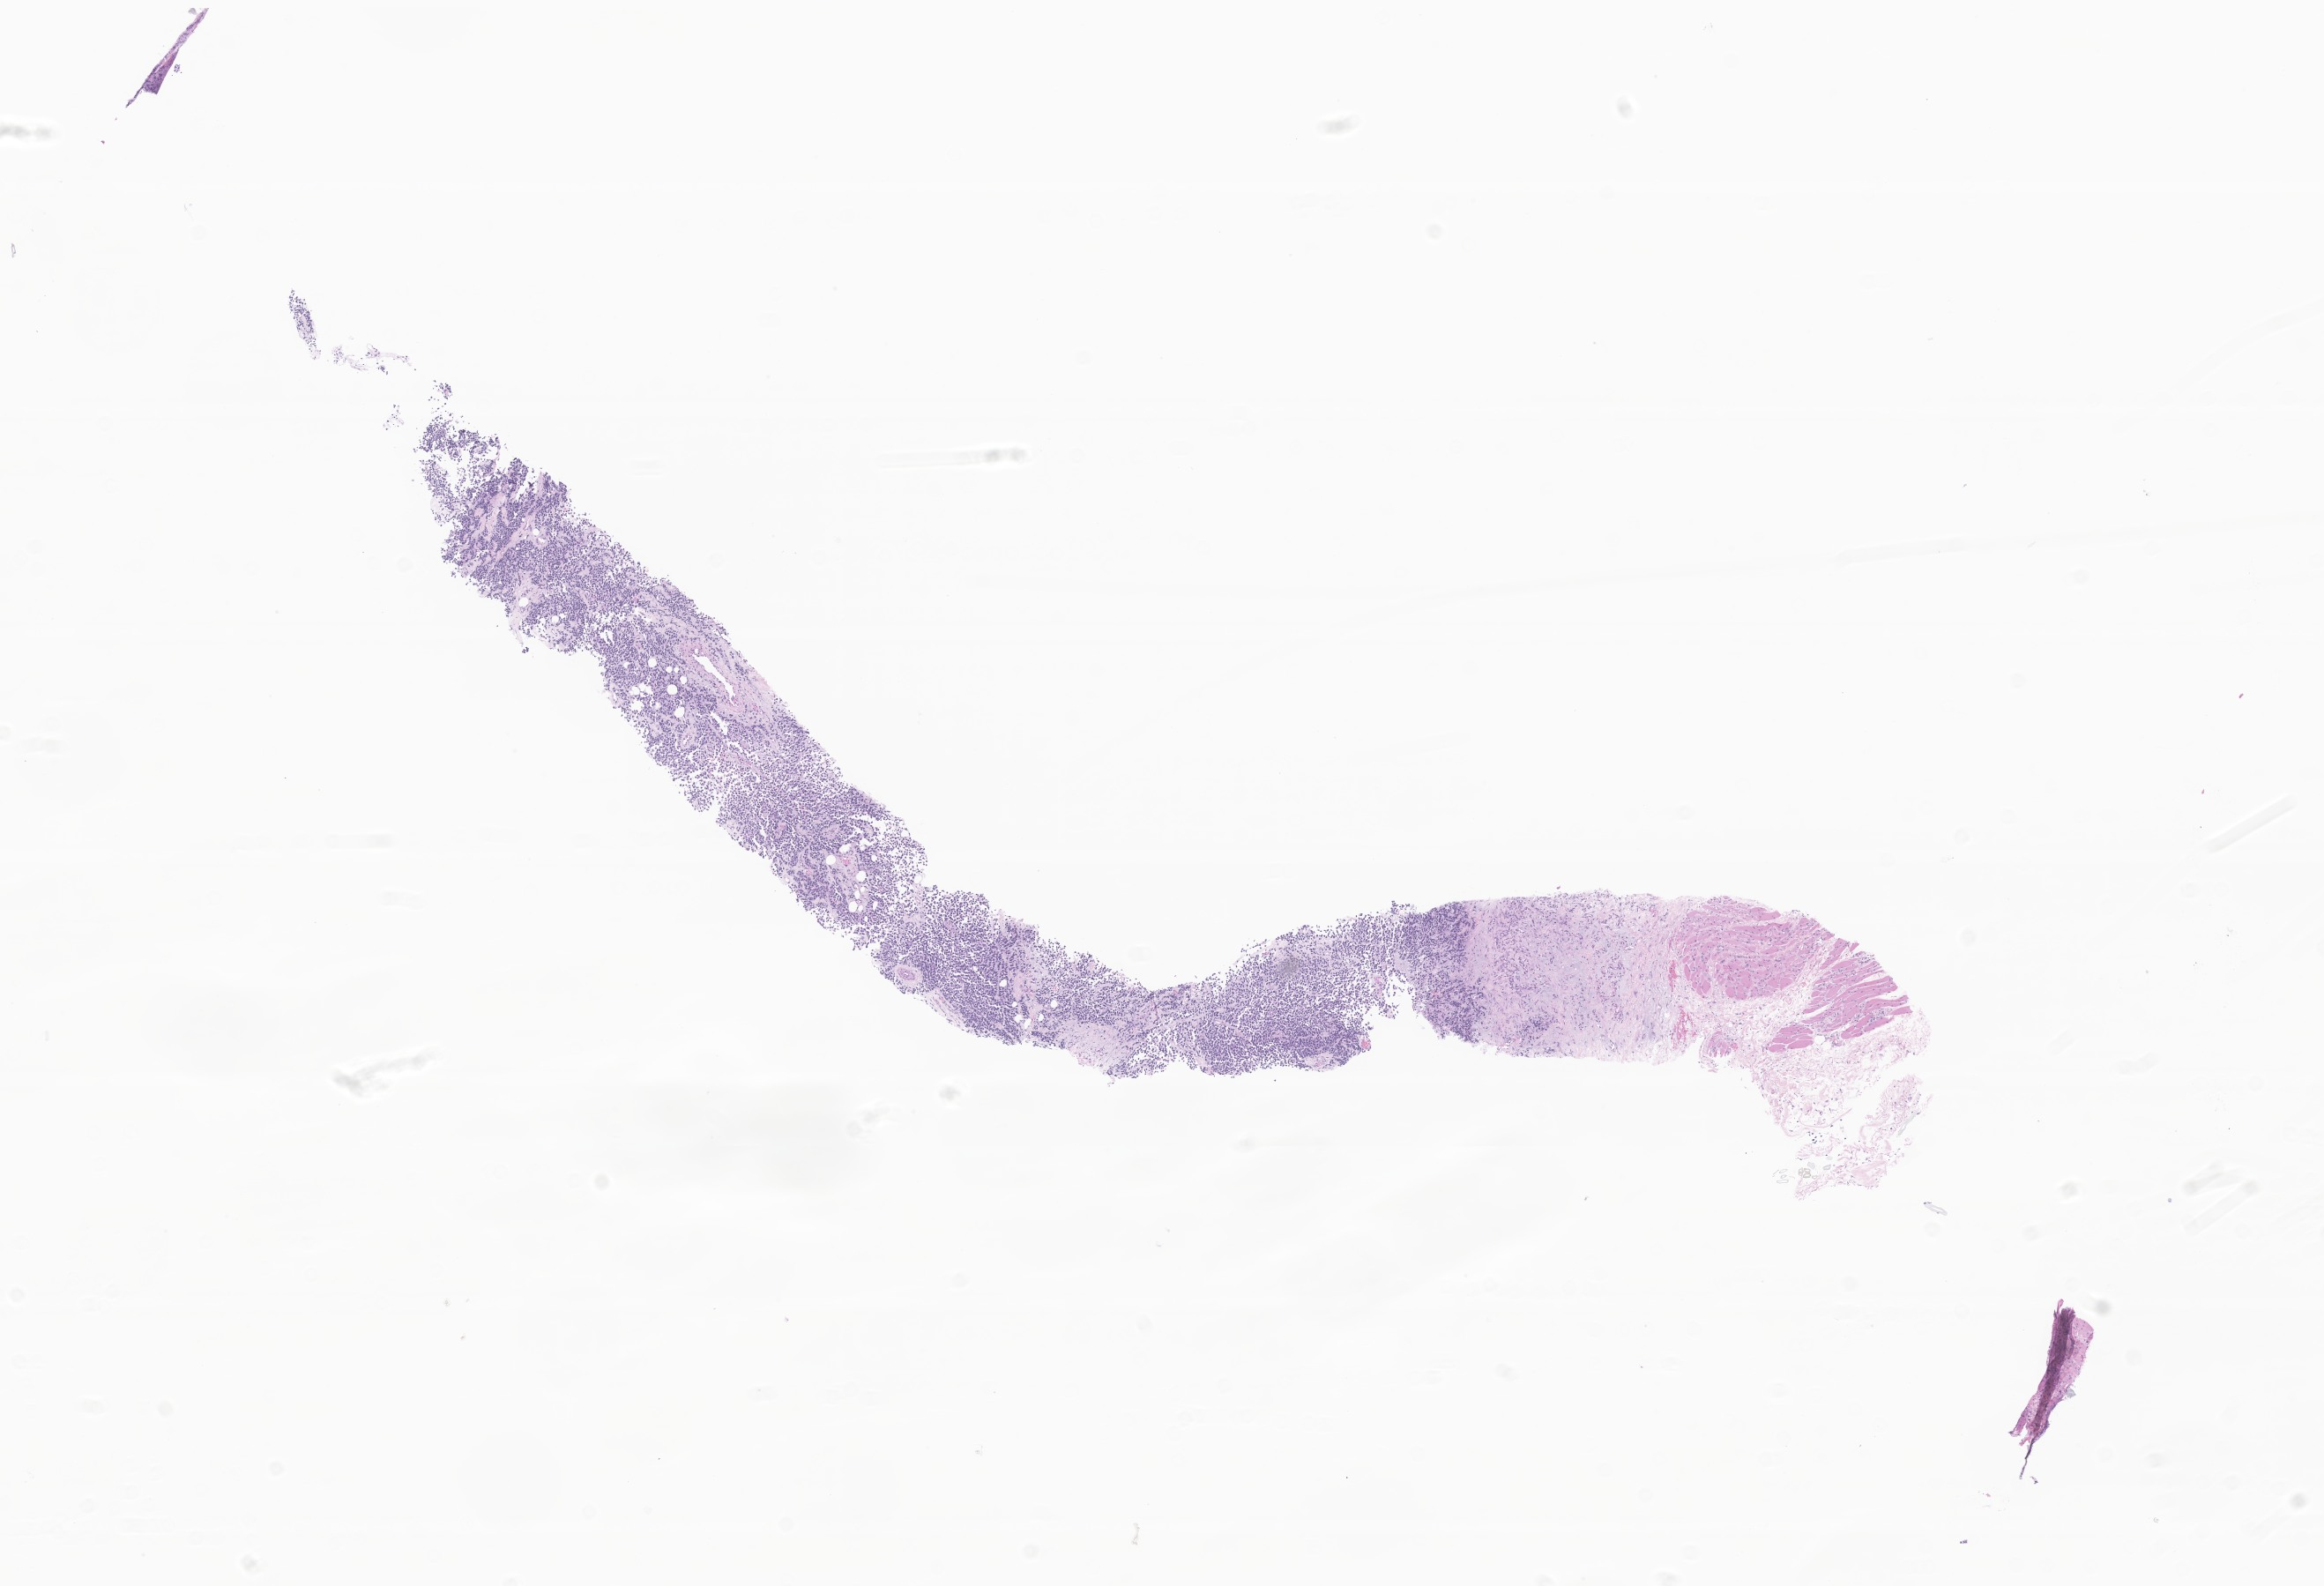
Digitized haematoxylin and eosin-stained section of tumor tissue from the pelvis — shown as a low-resolution overview of the whole scanned area (about 11.1 x 7.6 mm). Formalin-fixed, paraffin-embedded (FFPE) tissue. Patient: male, age 198 months (16 years 6 months).
* recorded diagnosis: Rhabdomyosarcoma, NOS